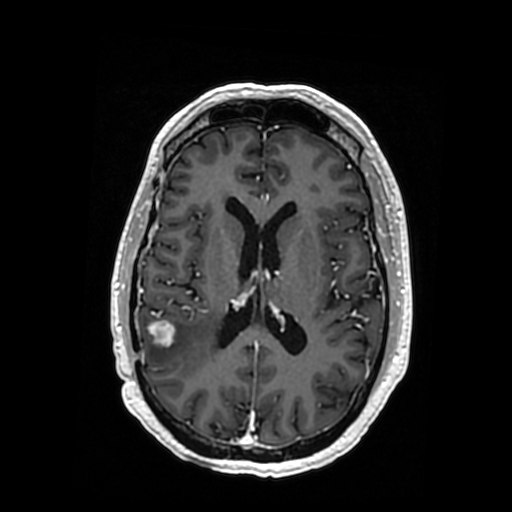
Brain MRI from a brain-tumour surgery series, one axial slice. Position 162 of 364 along the scan axis. T1-weighted post-contrast. 0.5 mm slice thickness. 512 × 512 image matrix, field of view 260 × 260 mm. From the clinical record (not read from this slice): histopathology: Oligodendroglioma; WHO grade: 3; IDH mutation: yes; tumour location: Right Posterior Temporal Inferior Parietal.
Outlined on this slice (expert manual segmentation):
- tumour: bounding box (x1, y1, x2, y2) in pixels: (149, 320, 177, 346)